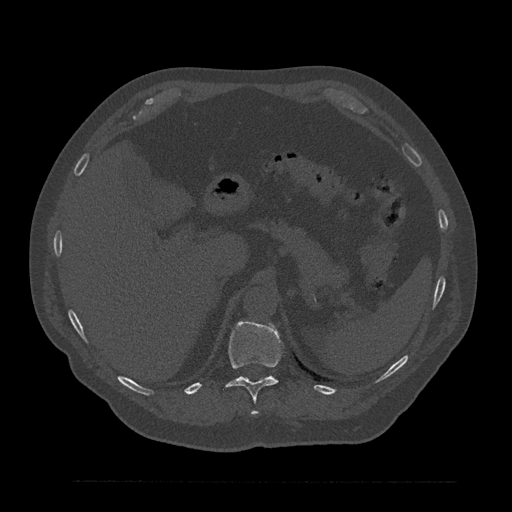
CT including the spine, one axial slice; slice 285 of 797 in the series (ordered by position); 120 kVp; bone window (W 1800 / L 400 HU); 512 × 512 image matrix, field of view 430 × 430 mm. Patient: male, 61 years. Case-level facts recorded for this patient, not image findings: primary cancer: prostate.
Annotated regions visible in this slice (semi-automatic segmentation, software-assisted and operator-edited):
- T11 vertebra: bounding box [x1, y1, x2, y2] px = [225, 321, 281, 415]